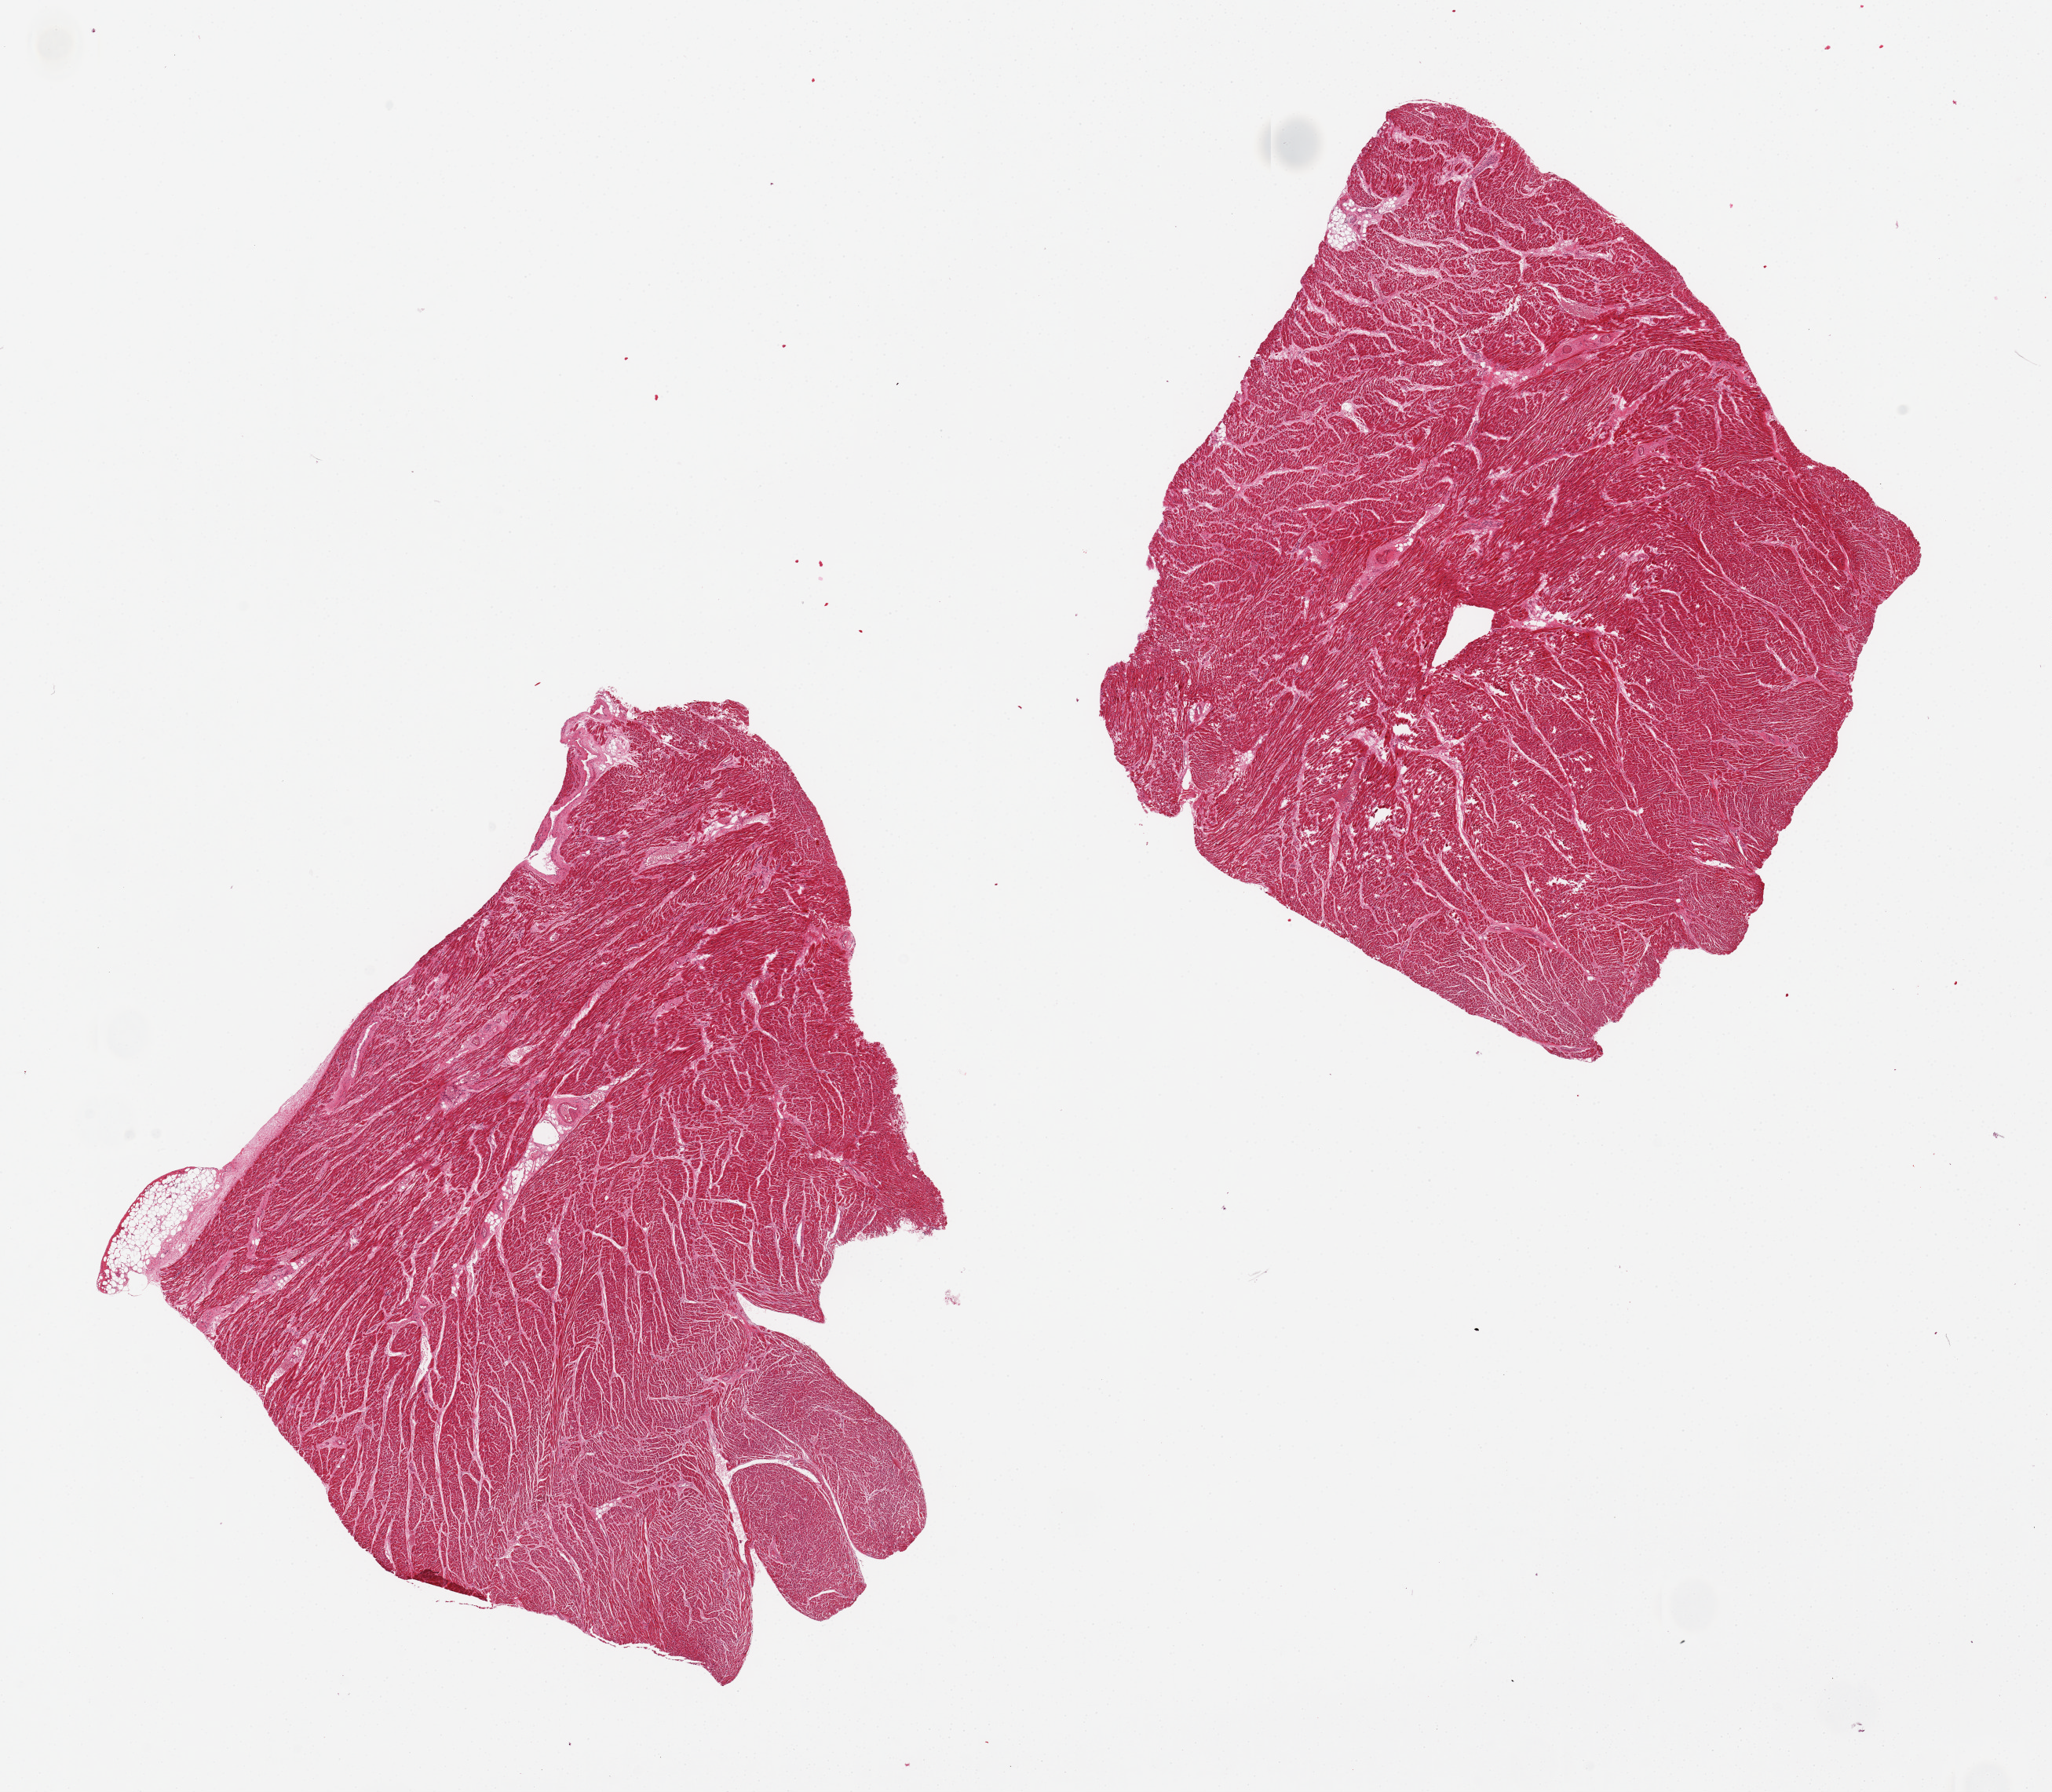
Haematoxylin and eosin whole-slide image — whole scanned area (about 20.7 x 18.1 mm, from a 20x scan) shown as a low-resolution overview; PAXgene-fixed paraffin-embedded (PFPE) section; target tissue: heart; donor tissue sample. Female donor.
Review note (as recorded): 2 pieces, minimal interstitial fibrosis.